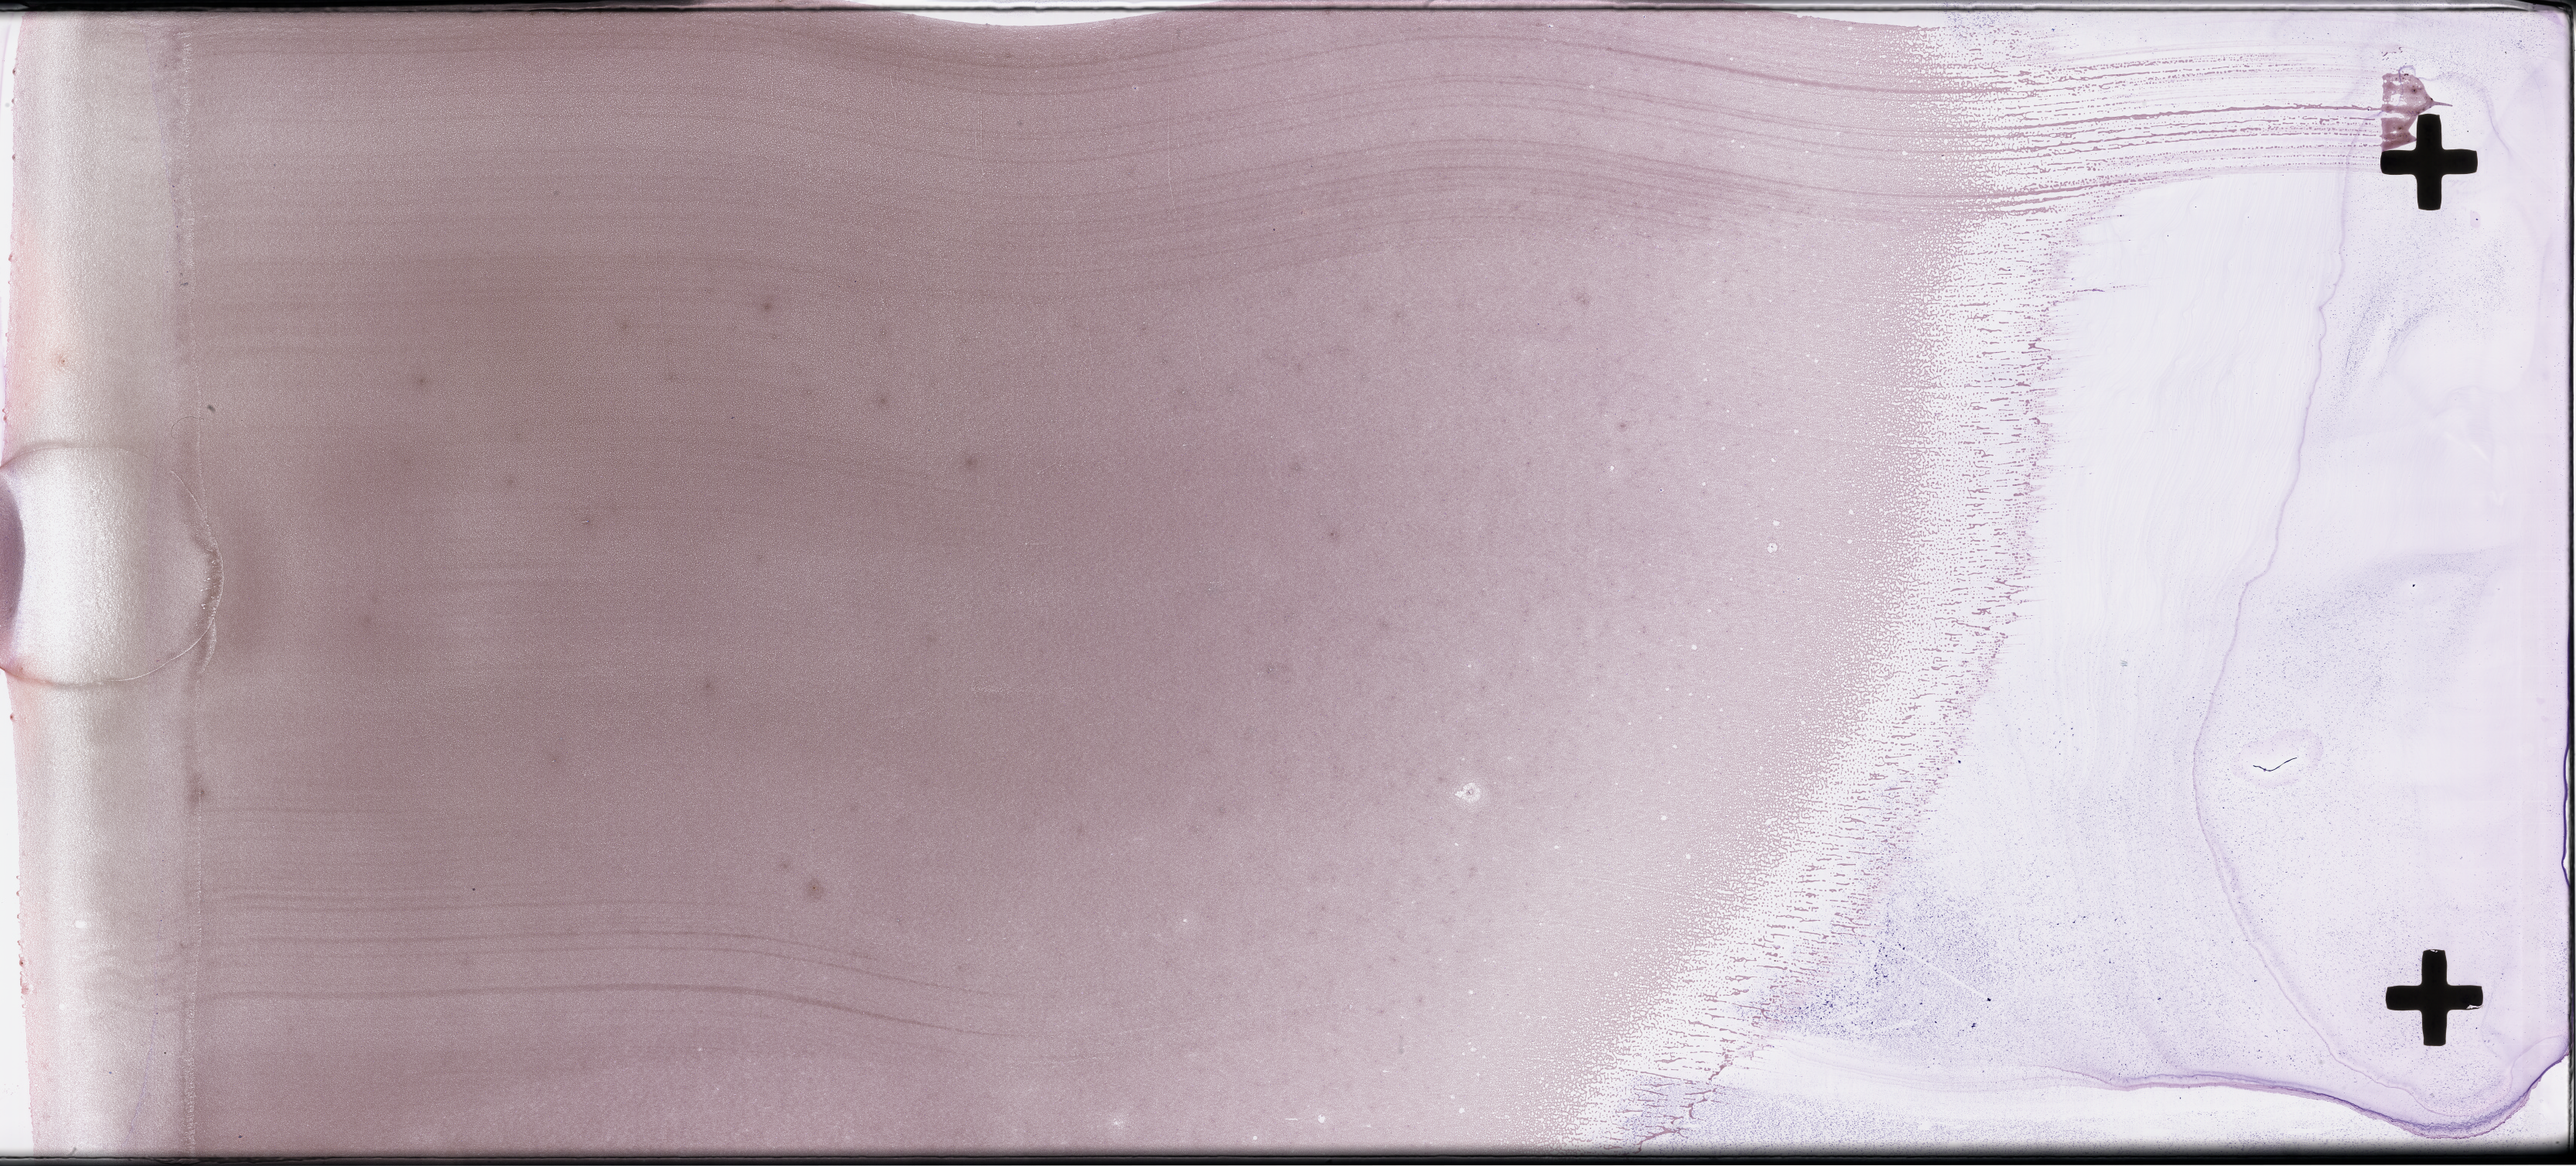
Whole-slide image of a whole blood smear, Wright–Giemsa stain — whole scanned area (about 53.8 x 24.3 mm) shown as a low-resolution overview; specimen time point: collected at baseline (before treatment). Patient sex: male.
• patient diagnosis: Plasma Cell Myeloma